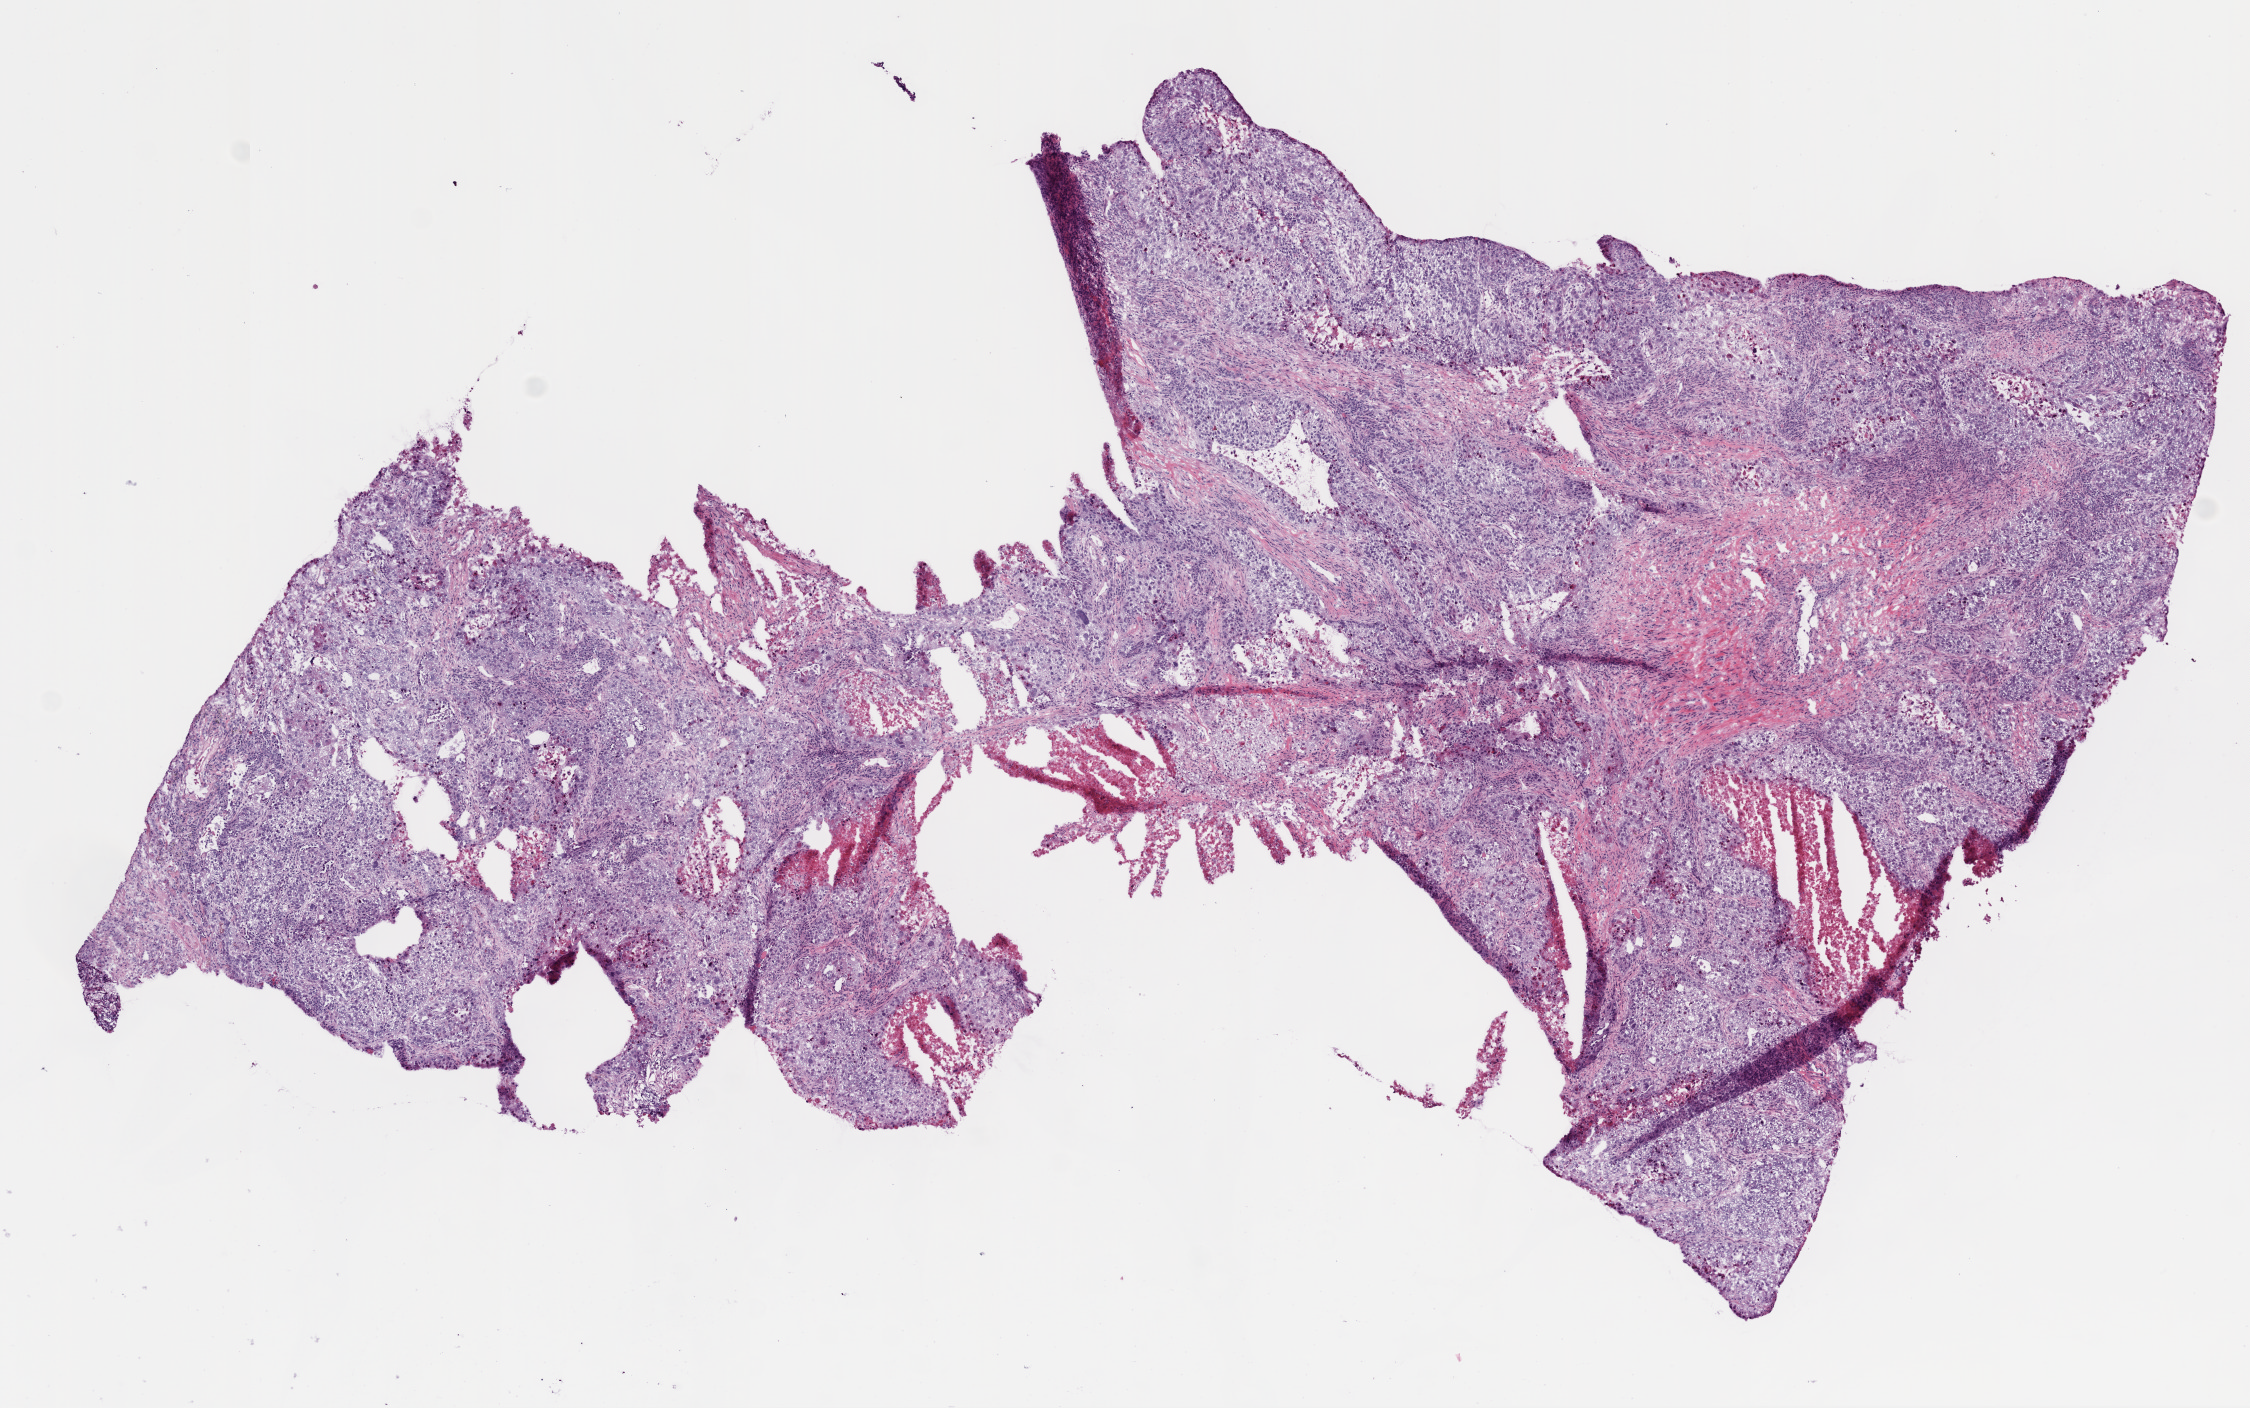
Digitized H&E tissue section (whole slide) — whole scanned area (about 9.0 x 5.6 mm) shown as a low-resolution overview. Frozen section. Sample: primary tumour, lung. Patient: female, age at initial diagnosis 59 years. Slide review estimates, as recorded: tumour cells 82%, tumour nuclei 75%, normal cells 0%, stromal cells 10%, necrosis 8%.
AJCC pathologic stage: IA. Laterality: right. Histologic diagnosis: Squamous cell carcinoma, NOS.